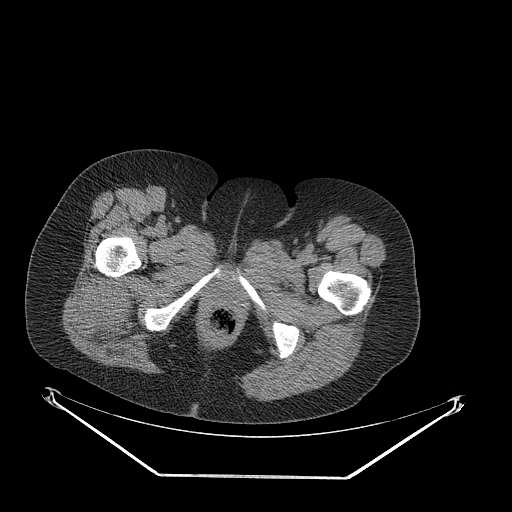
CT of an extremity soft-tissue mass (from a PET/CT study), one axial slice; position 57 of 257 along the scan axis; reconstruction kernel STANDARD; 140 kVp; soft-tissue window (W 400 / L 40 HU); 3.75 mm slice thickness; 512 × 512 image matrix, field of view 500 × 500 mm. Female patient. From the clinical record (not read from this slice): histological type: synovial sarcoma; grade: intermediate; site of the primary tumour: right buttock.
Outlined on this slice (expert contour drawn on MRI and transferred to this co-registered scan by the dataset authors):
- gross tumour volume including surrounding oedema: bounding box <80,272,142,350> (left, top, right, bottom; pixels)
- gross tumour volume (mass): <80,272,138,337>